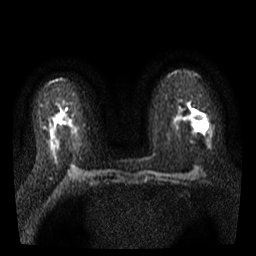
Breast MRI, one axial slice. Position 17 of 35 along the scan axis. Diffusion-weighted series; image 2 of 4 stored at this slice position (different b-values; order by instance number). 3 T. 5 mm slice thickness. 256 × 256 image matrix. Female patient.
Outlined on this slice (manually delineated by an expert):
- tumour on diffusion-weighted imaging: box from (x=188, y=111) to (x=207, y=131) px